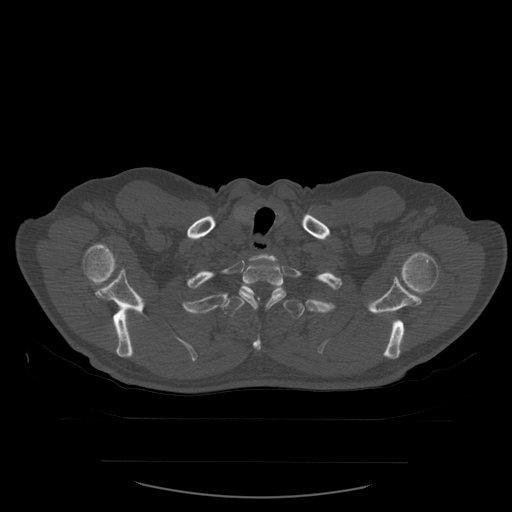
CT including the spine, one axial slice; position 470 of 590 along the scan axis; bone window (W 1800 / L 400 HU); 1.25 mm slice thickness; 512 × 512 image matrix, field of view 479 × 479 mm. Patient age 71 years. From the clinical record (not read from this slice): primary cancer: lung; vertebrae with lytic lesions (as recorded): T1, T2, L5, S1.
Annotated regions visible in this slice (semi-automatic segmentation, software-assisted and operator-edited):
- T1 vertebra: bounding box [x1, y1, x2, y2] px = [250, 254, 281, 270]
- T2 vertebra: [239, 260, 287, 309]
- T3 vertebra: [221, 288, 305, 351]